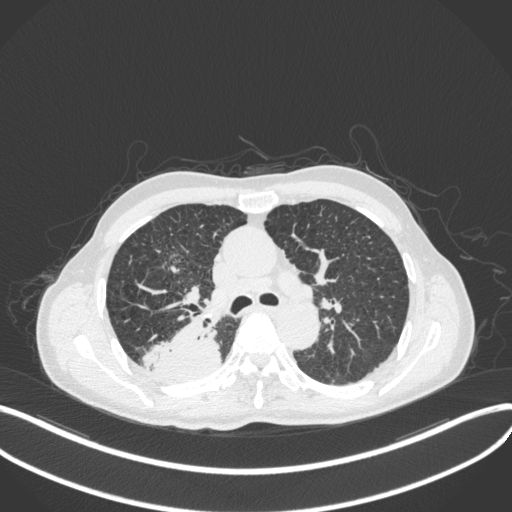
Chest CT, one axial slice; reconstruction kernel B31f; 120 kVp; lung window (W 1500 / L -600 HU); 1 mm slice thickness; 512 × 512 image matrix, field of view 400 × 400 mm. Patient: male, 79 years. From the clinical record (not read from this slice): clinical TNM (as recorded): T3 N0 M0.
Structures marked on this image (rectangle marked by the reading radiologist):
- lung tumour (recorded histology: adenocarcinoma): bounding box (x1, y1, x2, y2) in pixels: (139, 314, 222, 383)